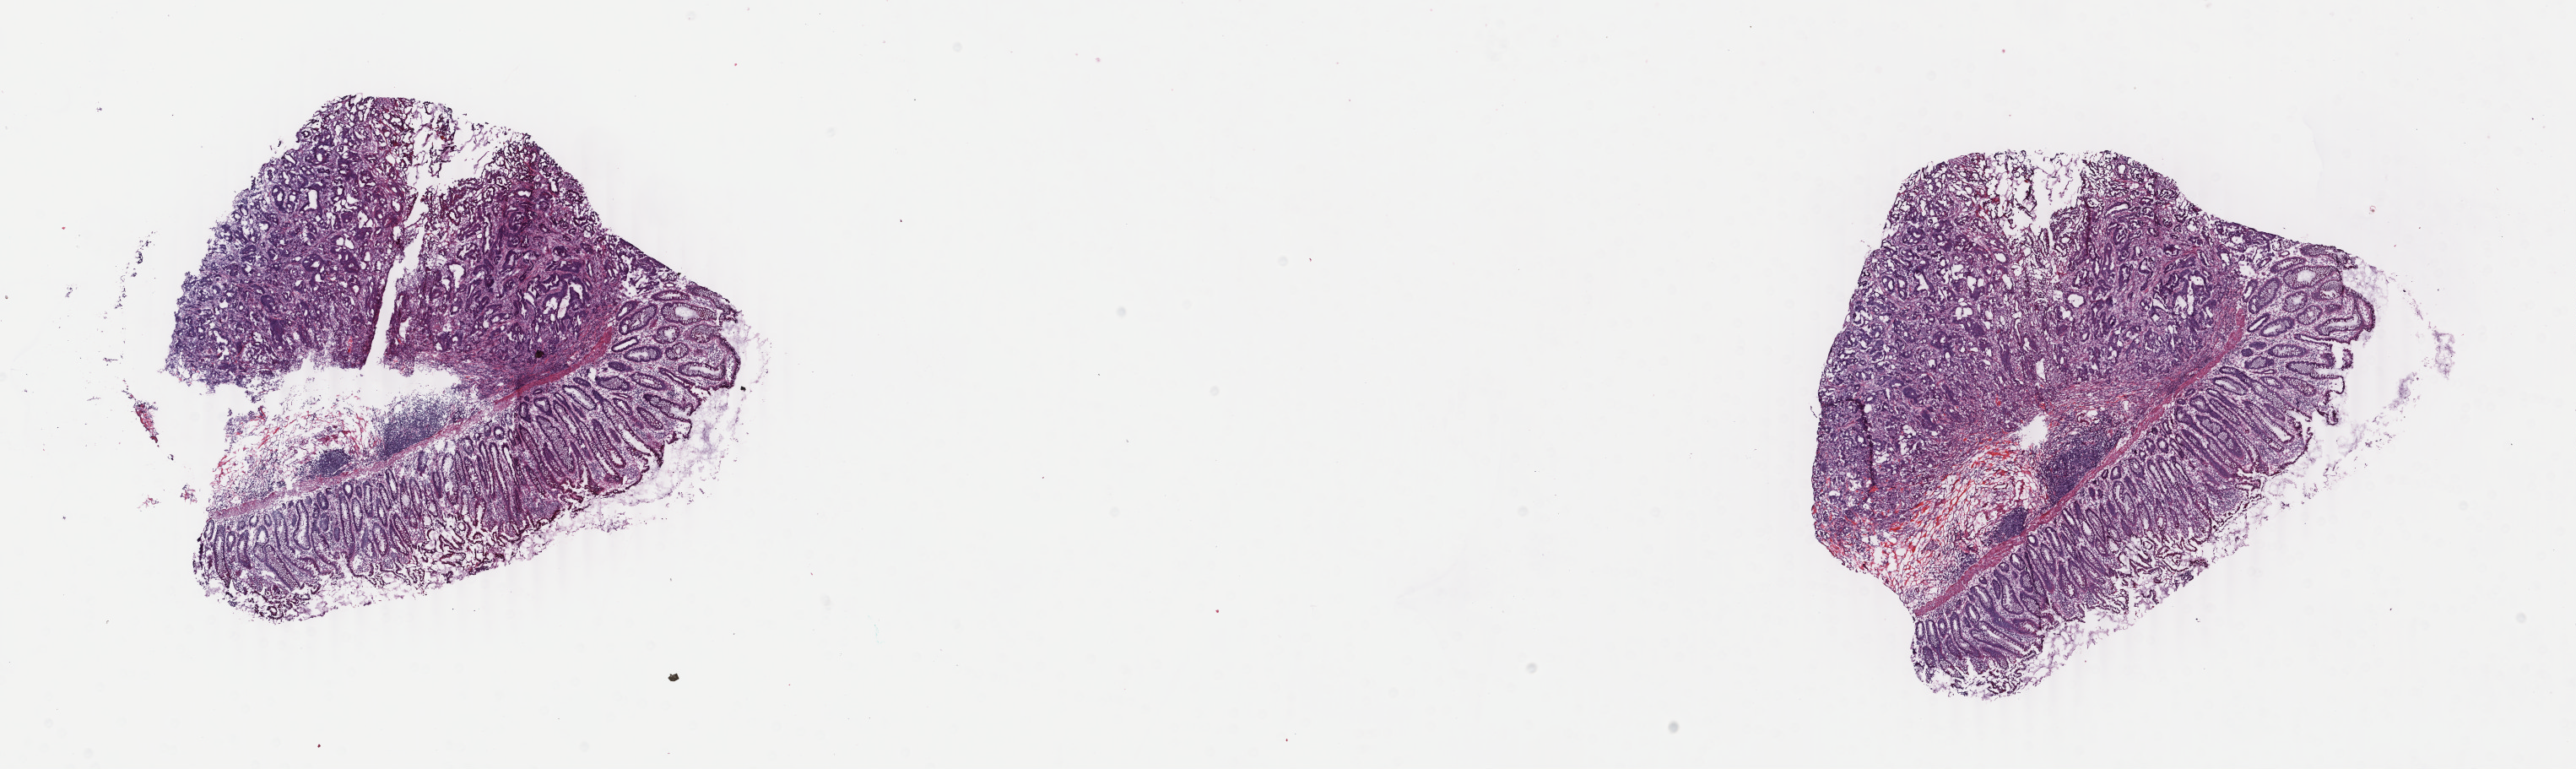
Whole-slide histology image, H&E — low-resolution overview of the scanned area, about 24.3 x 7.2 mm (slide scanned at 40x), frozen section, primary tumour sample from the colon. Male, age 68 years at initial diagnosis. Pathologist review of this section (percent, as recorded): tumour cells 60%, tumour nuclei 60%, normal cells 25%, stromal cells 14%, necrosis 1%. Infiltration values recorded for this section: lymphocyte infiltration 3%, monocyte infiltration 1%, neutrophil infiltration 4%.
Histologic diagnosis: Adenocarcinoma, NOS (ascending colon). TNM: T3 N0 M0. Lymph nodes positive (case pathology): 0 of 12 examined. AJCC pathologic stage: II (5th edition).